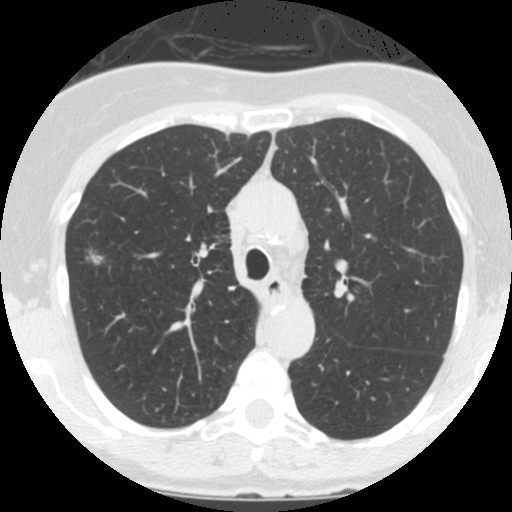
Chest CT (low-dose screening protocol), one axial image, third screening round (two years after baseline), lung window (W 1500 / L -600 HU), 120 kVp, slice 45 of 146 in the series, 512 × 512 image matrix. Female, age 60 years at enrolment.
Expert reader's lesion annotation, bounding box [x1, y1, x2, y2] px = [68, 233, 116, 286]. The exam's reader record, not a measurement of the box and not confirmed to be the same lesion: non-calcified nodule or mass ≥4 mm, right upper lobe, 12 × 12 mm, smooth margins, ground glass attenuation, pre-existing on the prior screen: yes; interval growth: yes. Later outcome: lung cancer diagnosed 56 days after this screen — bronchiolo-alveolar adenocarcinoma, NOS, right upper lobe, well differentiated (G1), stage IA (AJCC 6th edition), 11 mm at pathology.